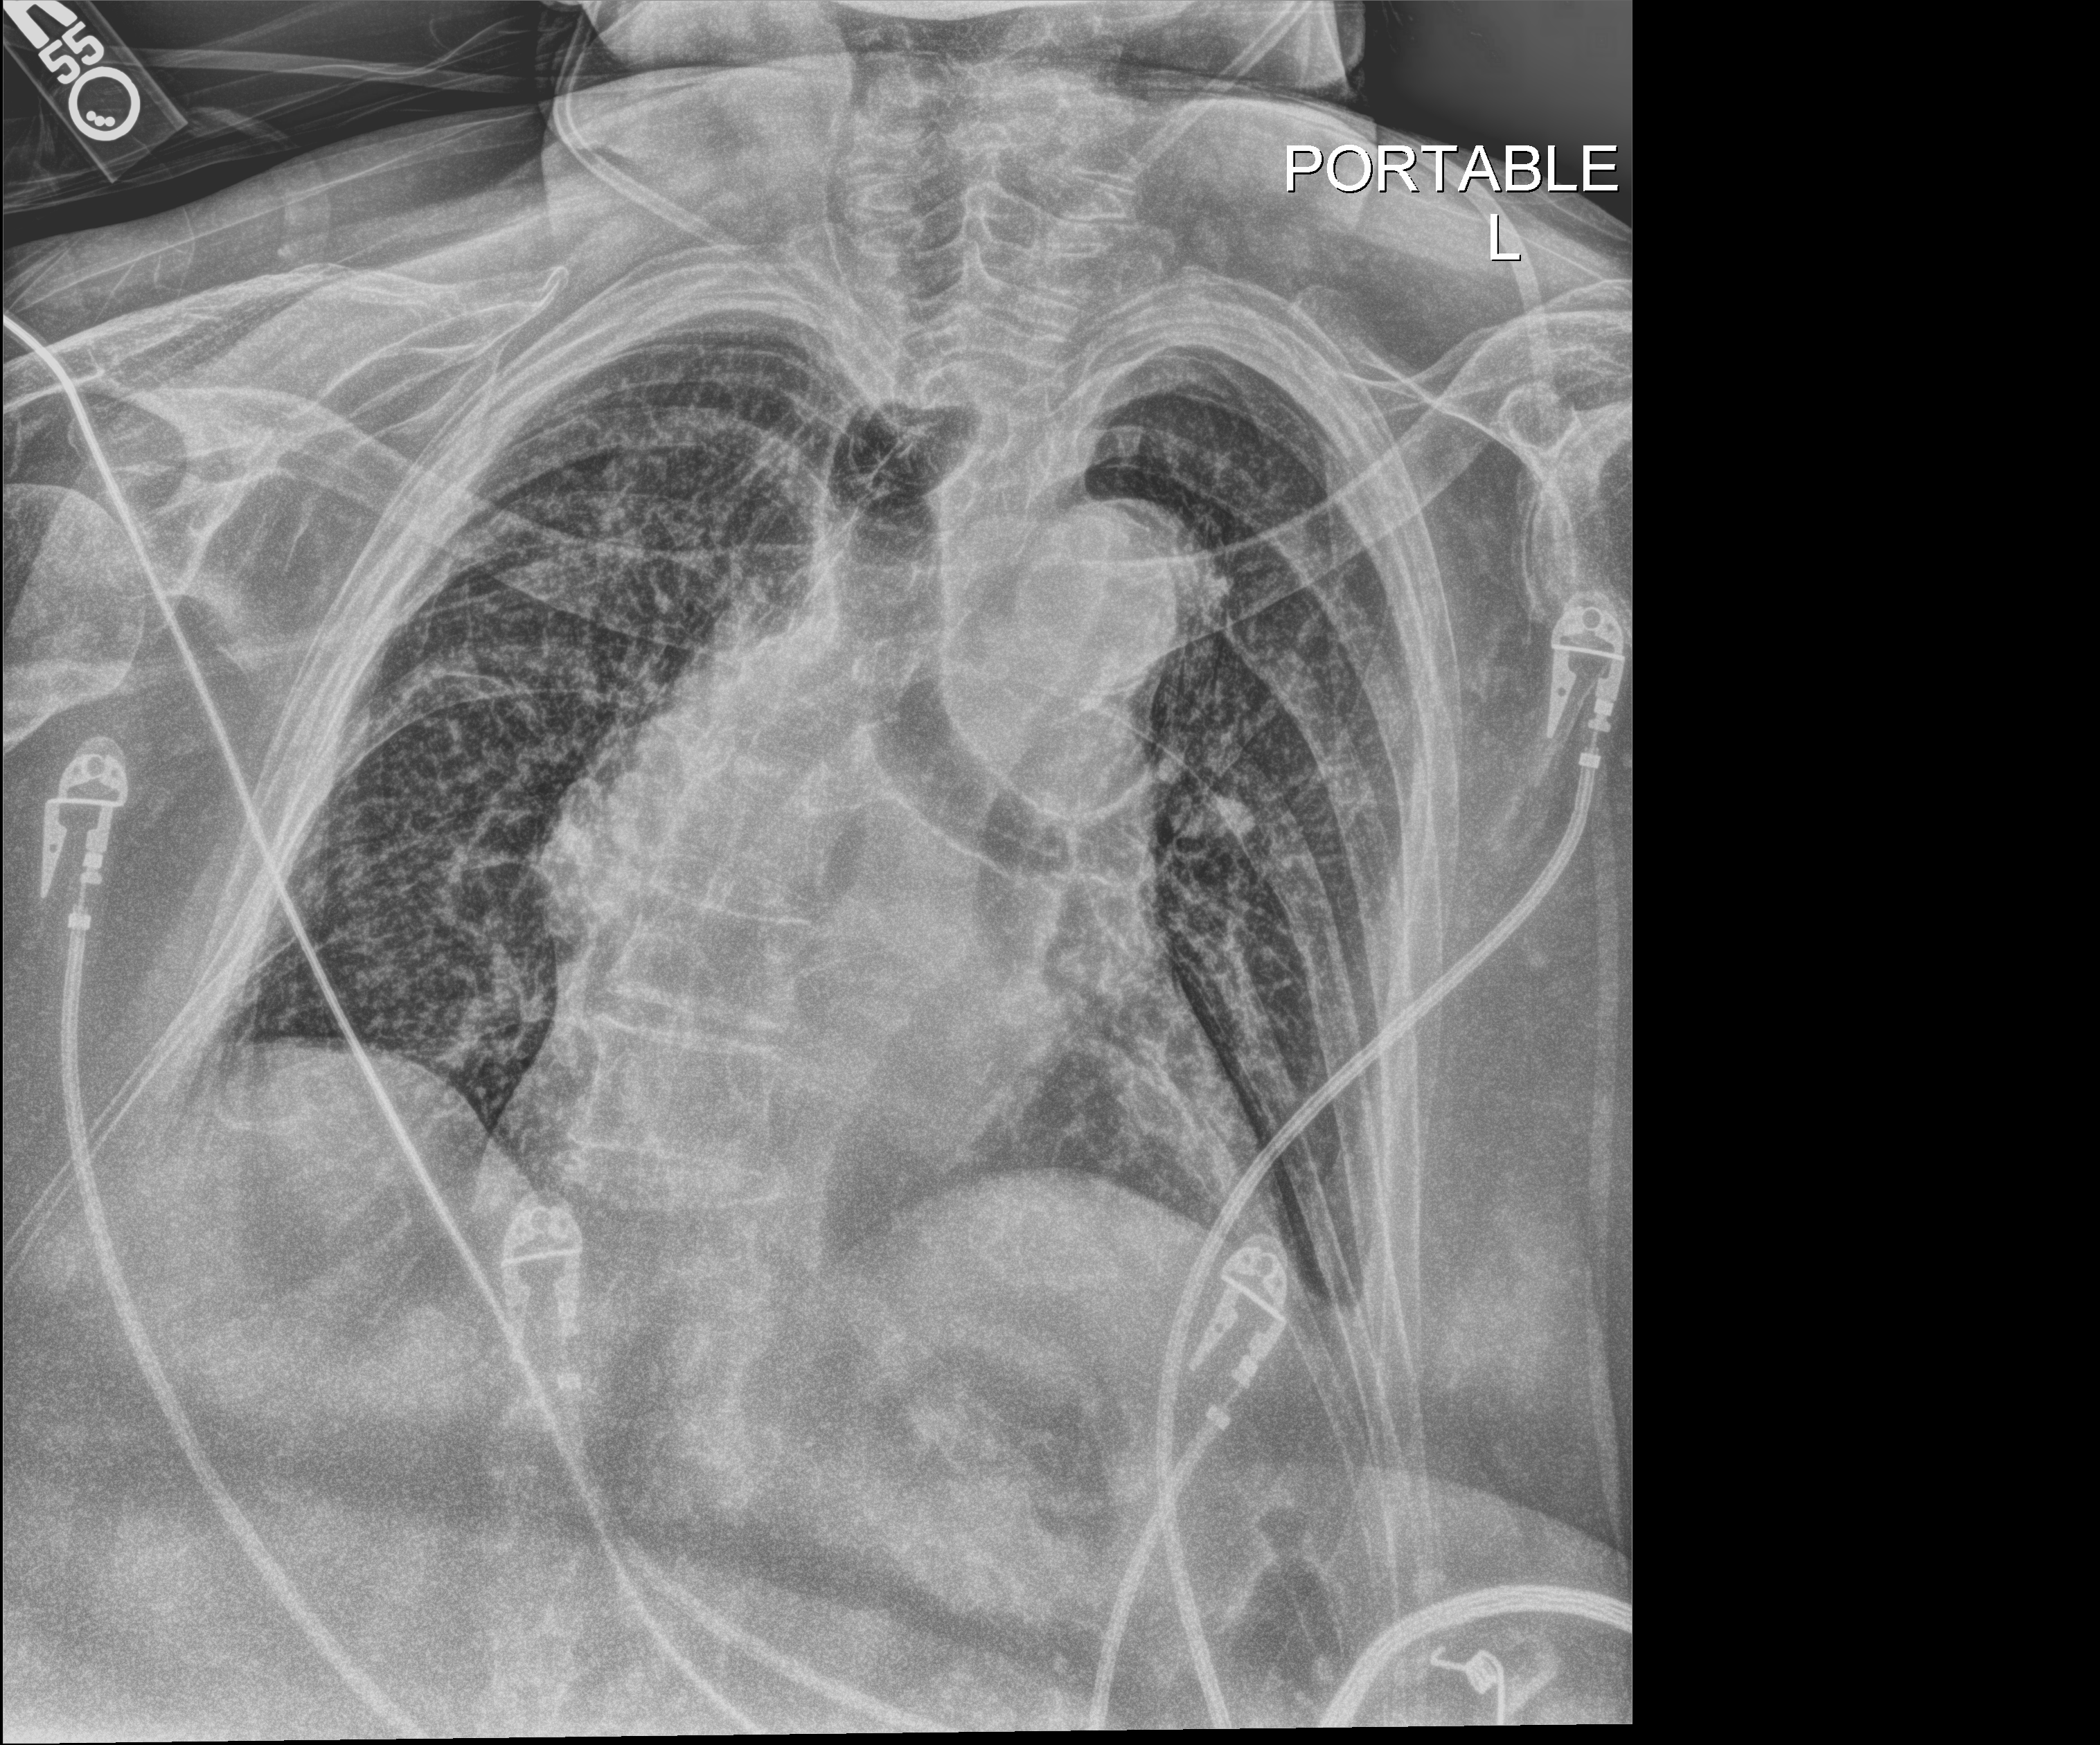
Portable chest radiograph. Female patient hospitalised with COVID-19, age 75–90 years.
From the hospital-stay record, not from the radiograph (when in the stay this image was taken is not recorded): mechanically ventilated during this hospital stay: no; admitted to intensive care during this hospital stay: yes.